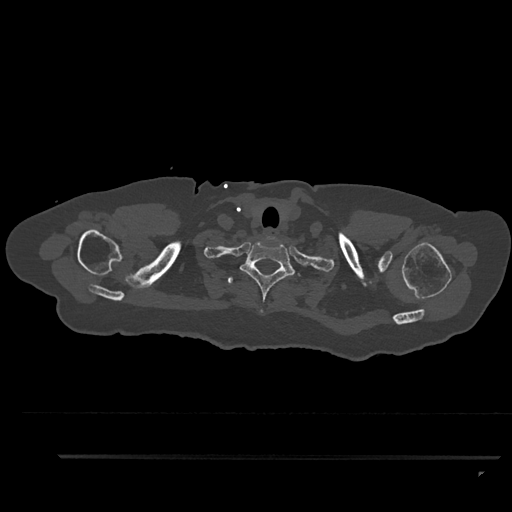
CT including the spine, one axial slice; slice 761 of 797 in the series (ordered by position); reconstruction kernel Br40s/3; bone window (W 1800 / L 400 HU); 0.5 mm slice thickness; 512 × 512 image matrix, field of view 408 × 408 mm. Female patient, age 44 years. Case-level facts recorded for this patient, not image findings: primary cancer: renal; vertebrae with lytic lesions (as recorded): L1.
Structures marked on this image (semi-automatic segmentation, software-assisted and operator-edited):
- T1 vertebra: bounding box <240,242,300,313> (left, top, right, bottom; pixels)
- T2 vertebra: <227,277,233,284>